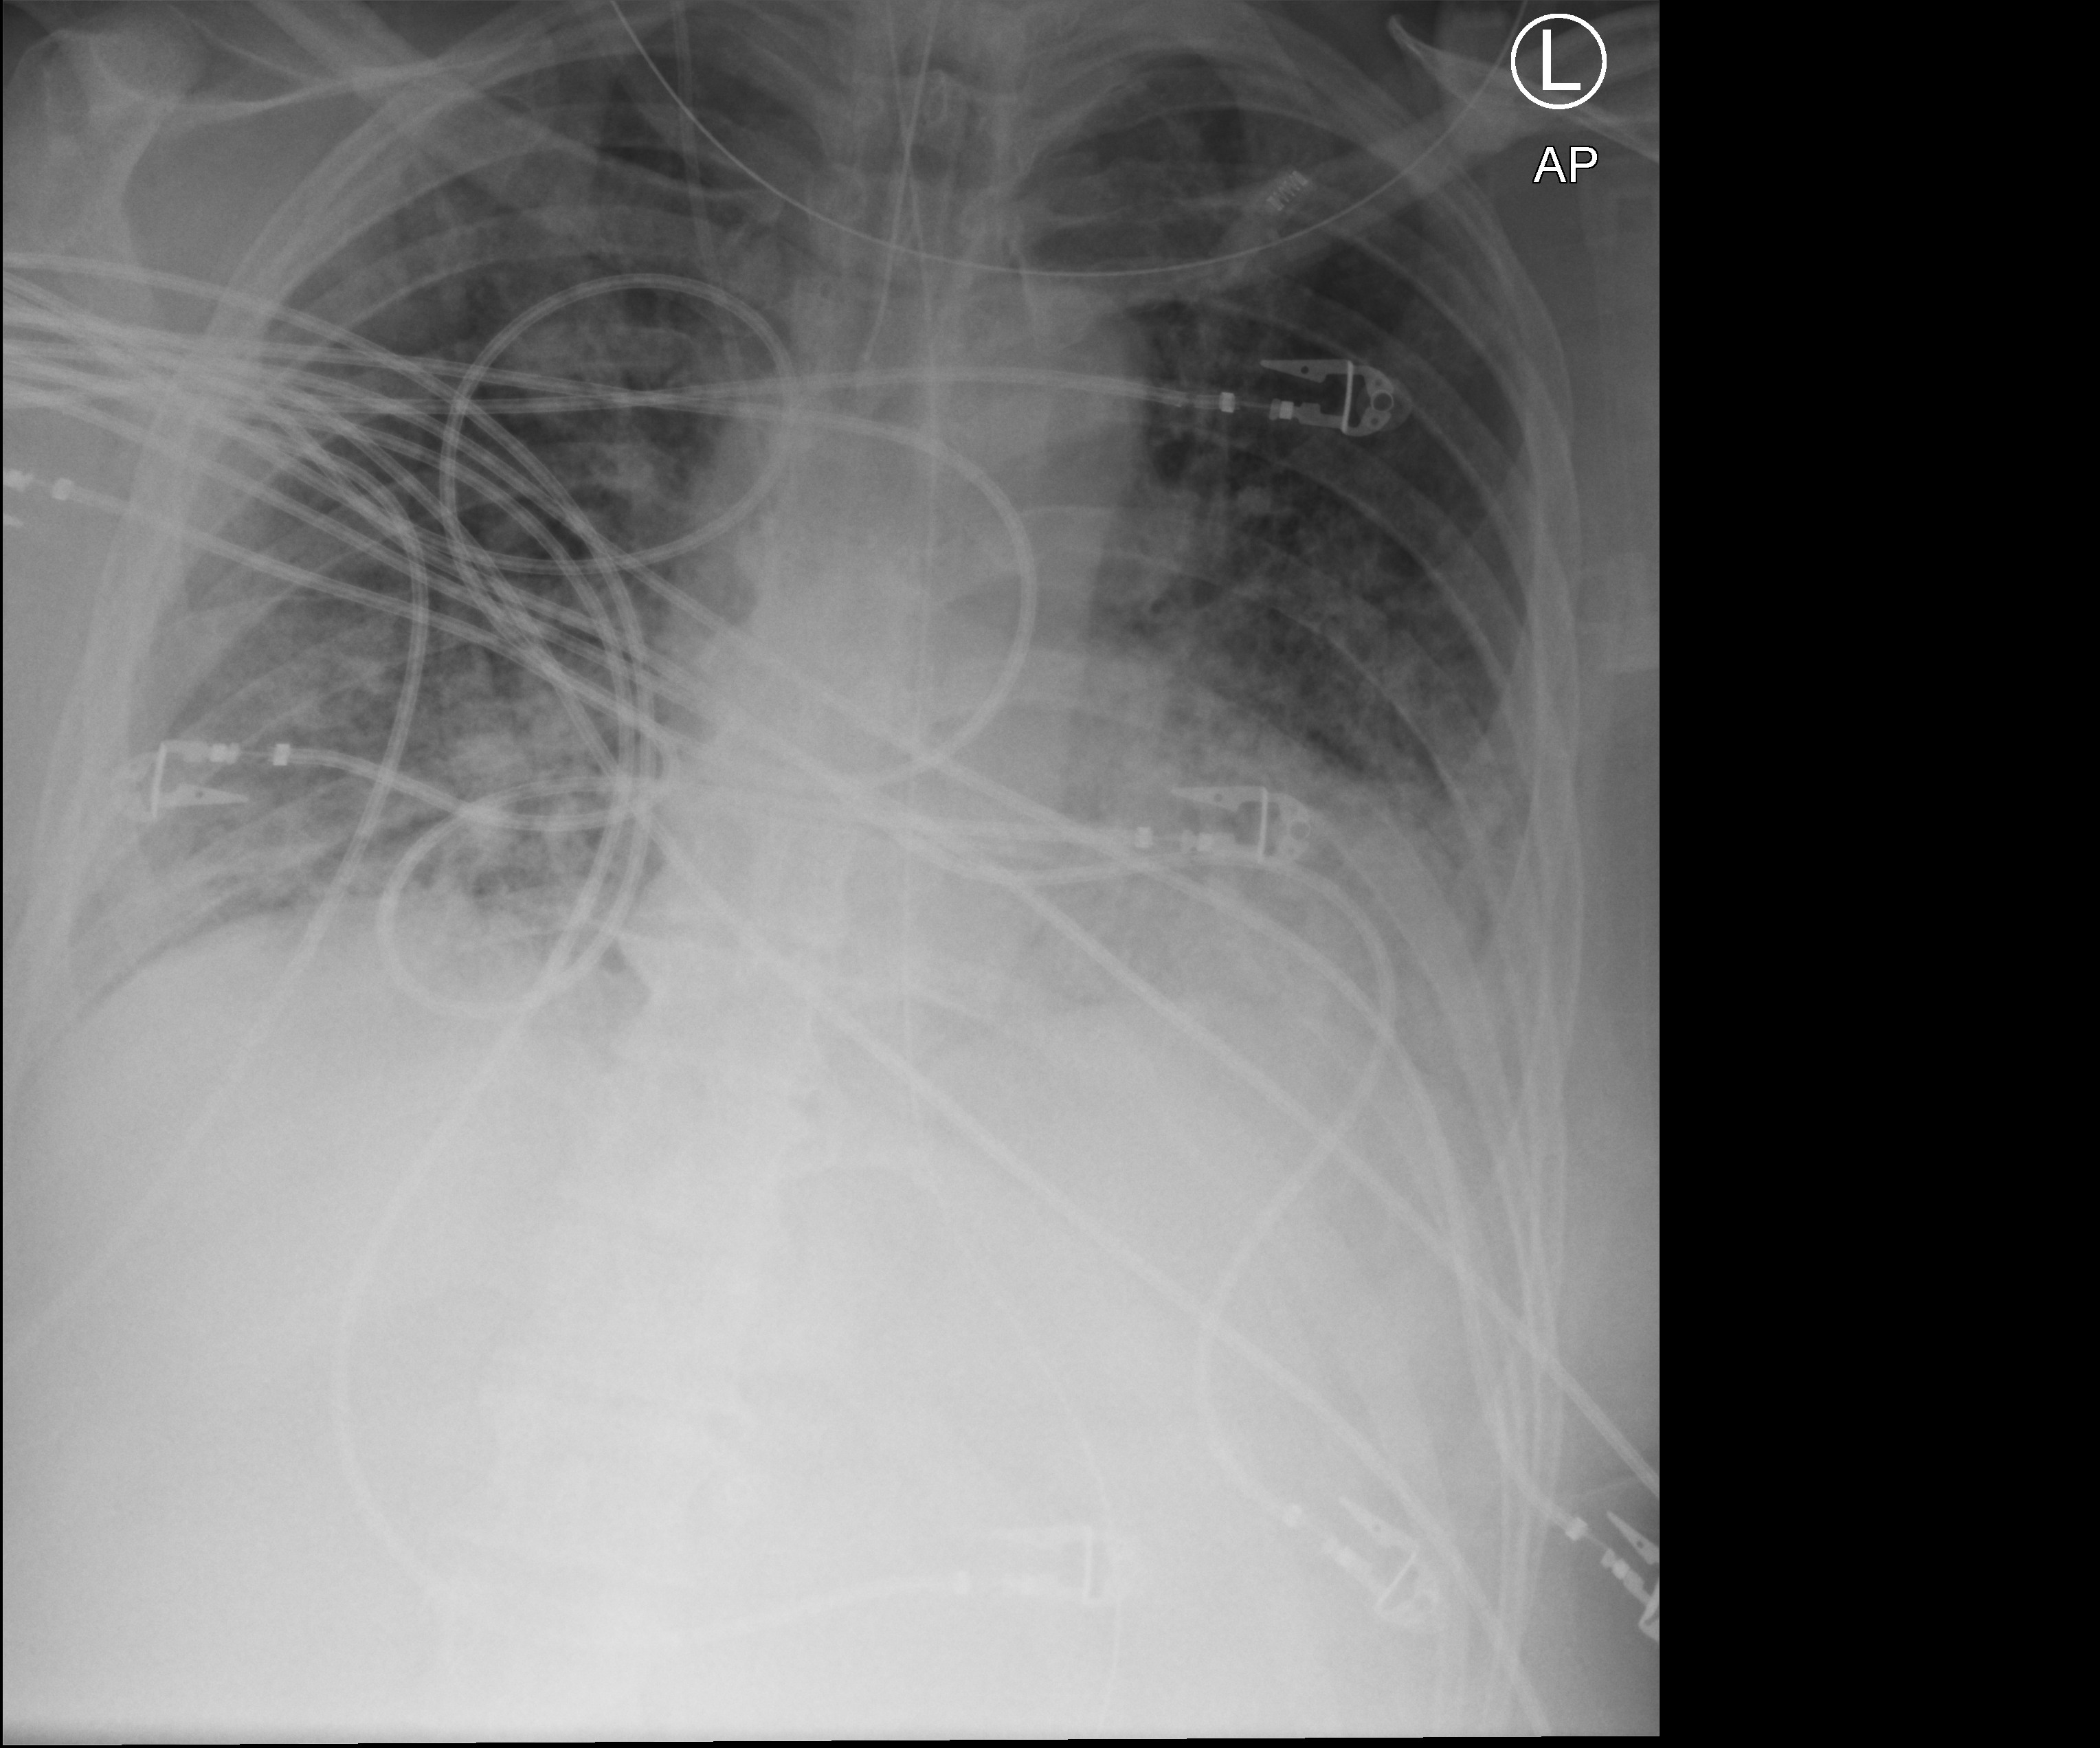
Bedside chest radiograph (computed radiography). Patient hospitalised with COVID-19; male, aged 60–74 years.
From the hospital-stay record, not from the radiograph (when in the stay this image was taken is not recorded): smoking status (admission record): former.